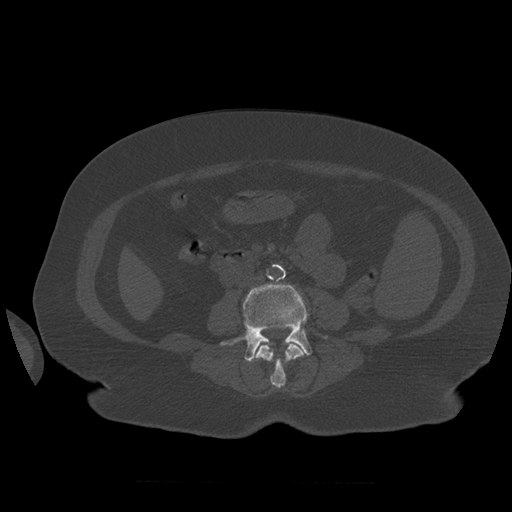
CT including the spine, one axial slice. Slice 215 of 399 in the series (ordered by position). Reconstruction kernel STANDARD. Bone window (W 1800 / L 400 HU). 1.25 mm slice thickness. 512 × 512 image matrix, field of view 404 × 404 mm. Patient age 81 years. From the clinical record (not read from this slice): primary cancer: renal; vertebrae with lytic lesions (as recorded): L1.
Annotated regions visible in this slice (semi-automatic segmentation, software-assisted and operator-edited):
- L3 vertebra: box from (x=255, y=341) to (x=305, y=388) px
- L4 vertebra: (x=221, y=284)–(x=312, y=362)